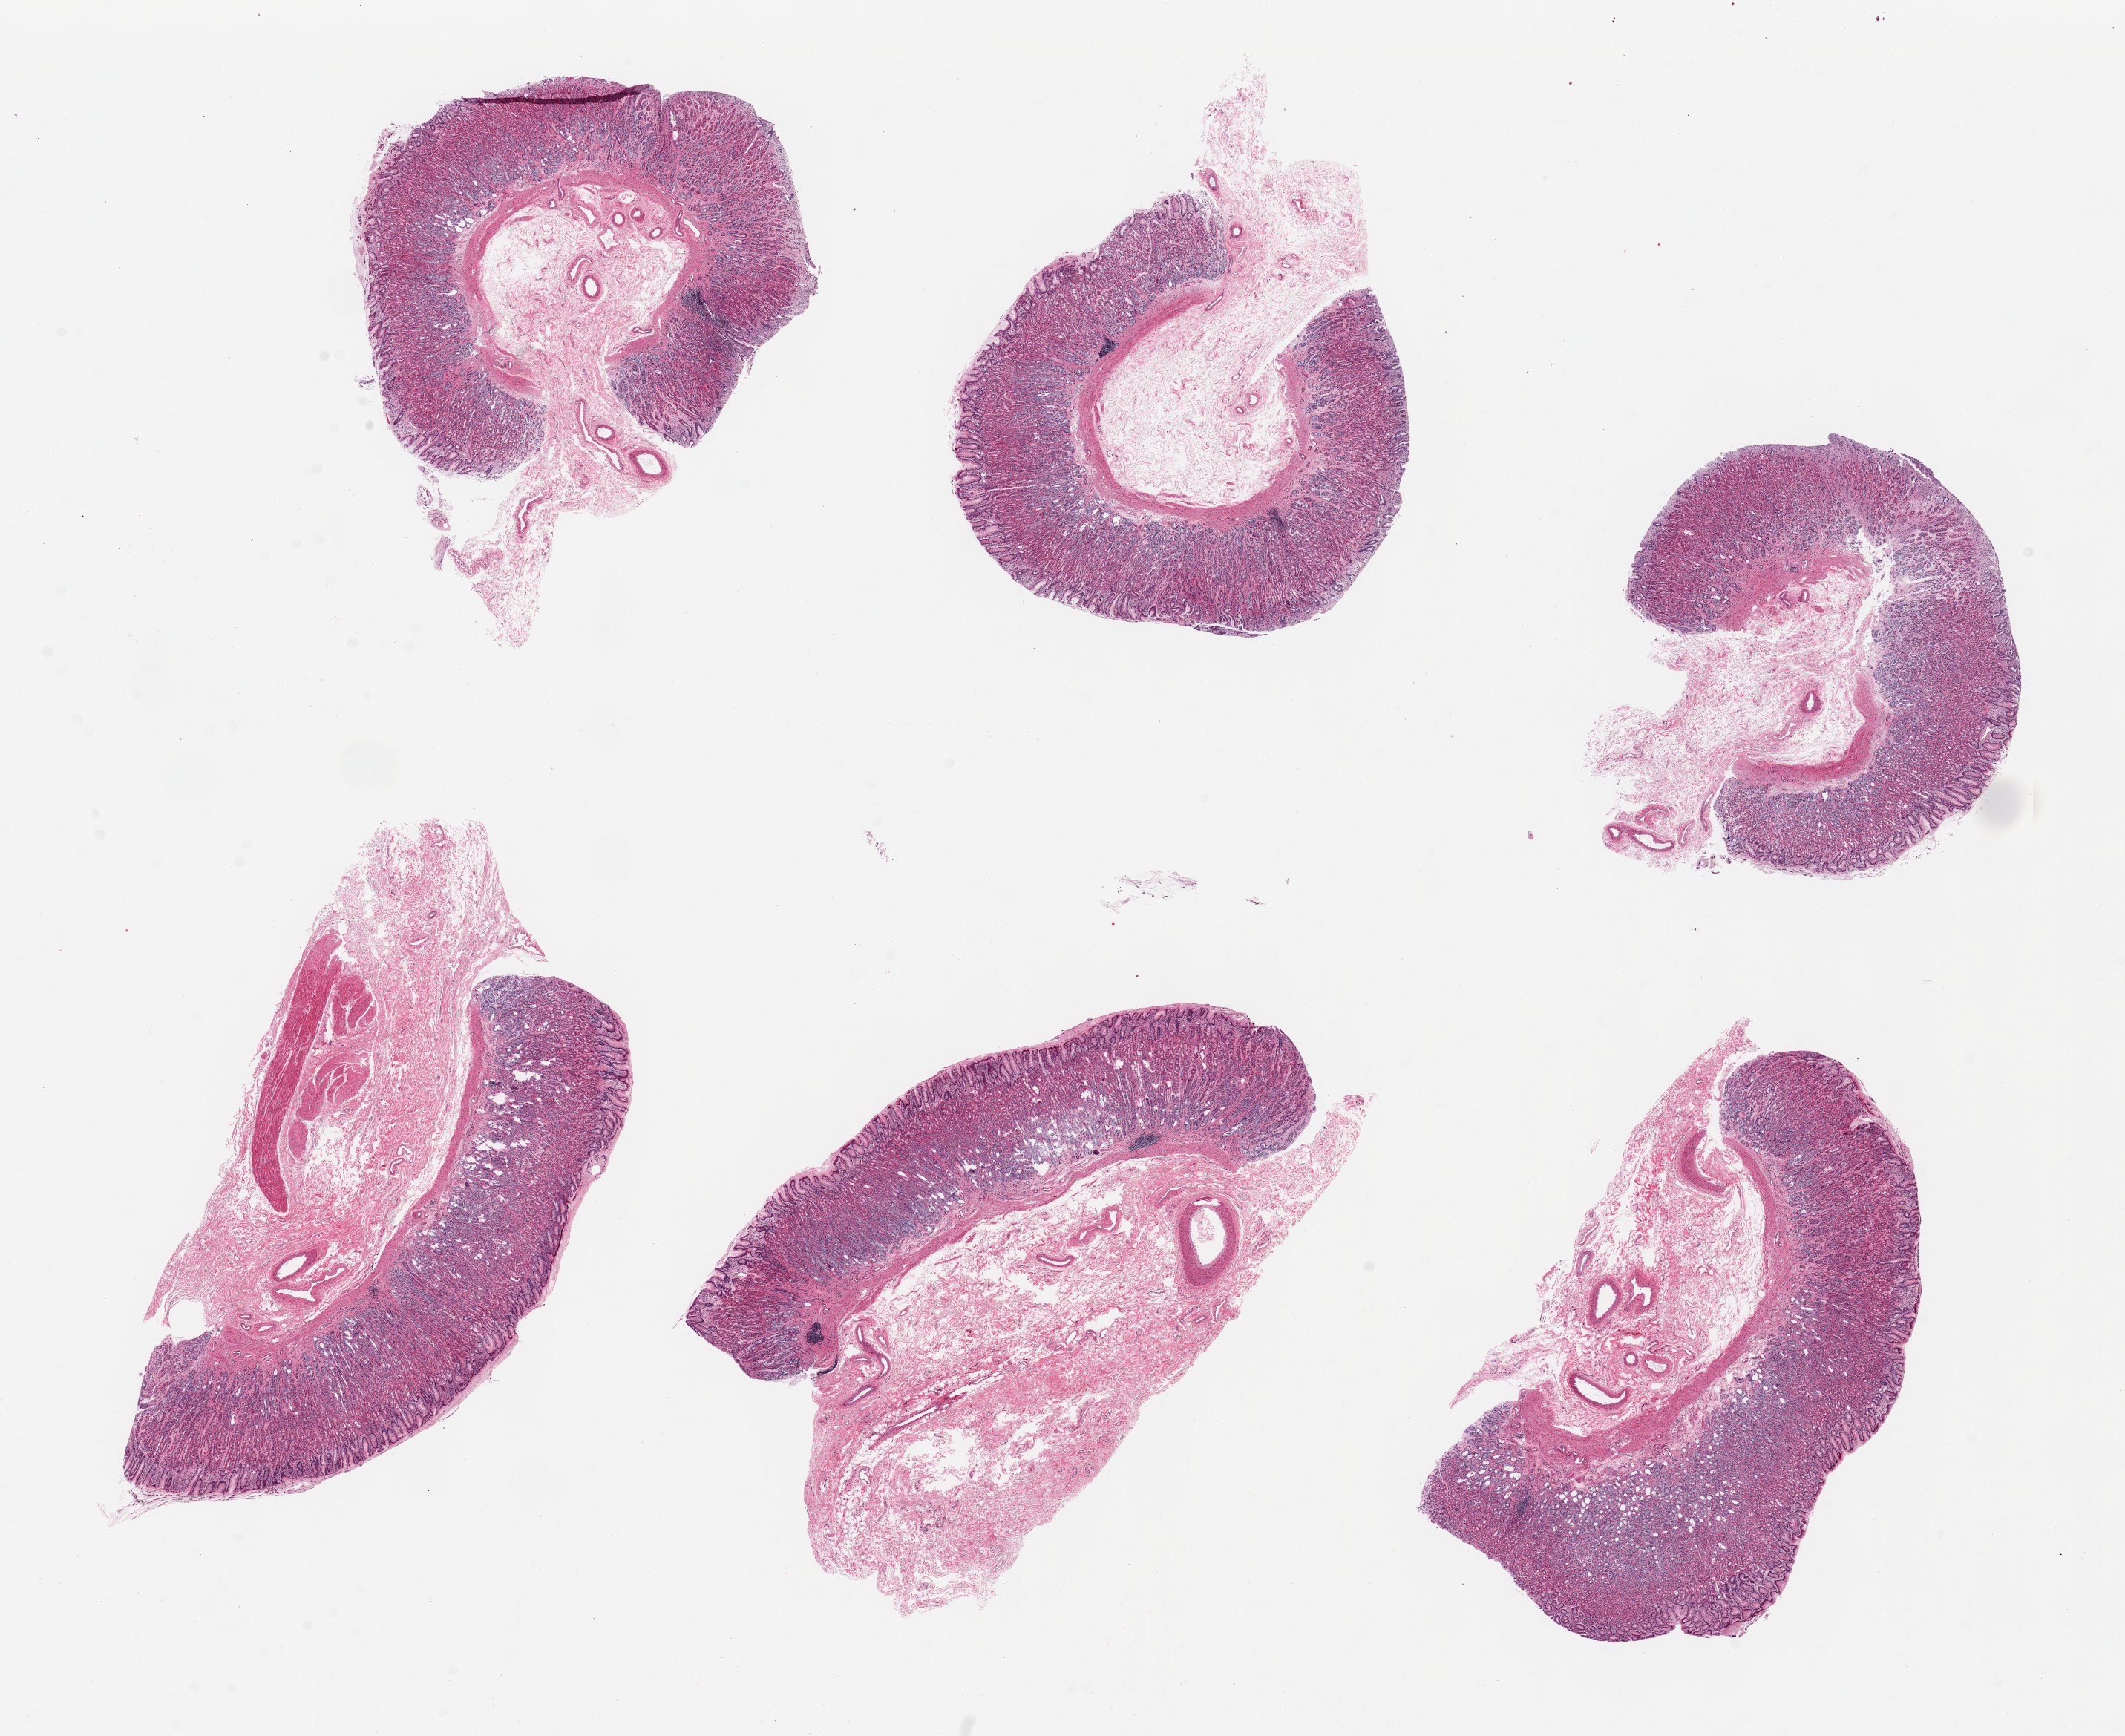
Digitized H&E-stained section, brightfield — whole scanned area (about 22.6 x 18.5 mm, acquisition: 20x scan) shown as a low-resolution overview. PAXgene-fixed, paraffin-embedded tissue. Target tissue: stomach. Tissue donor sample. Donor sex: female.
- reviewer comment on this tissue sample: 6 pieces, up to 8x4mm; mucosa well-preserved; 30-40% of thickness